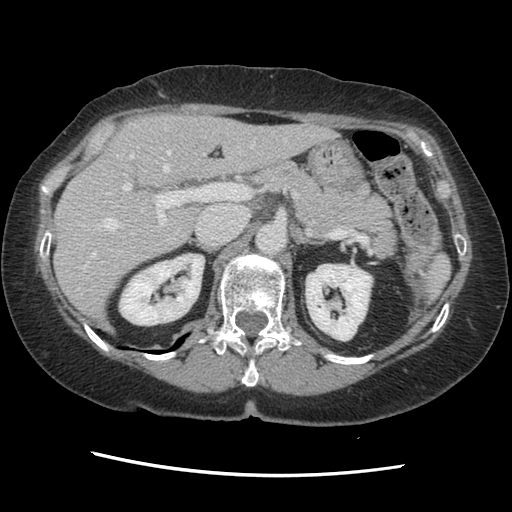
Contrast-enhanced abdominal CT, one axial slice; slice 85 of 141 in the series (ordered by position); 120 kVp; soft-tissue window (W 400 / L 40 HU); 2.5 mm slice thickness; 512 × 512 image matrix, field of view 330 × 330 mm. Female patient, age 61 years. Case-level facts recorded for this patient, not image findings: diagnosis: colorectal cancer liver metastases, imaged before liver resection.
Structures marked on this image (manually delineated by an expert):
- hepatic veins: bounding box [x1, y1, x2, y2] px = [82, 127, 287, 270]
- liver: [56, 114, 331, 316]
- planned liver remnant (the part of the liver to remain after resection): [56, 114, 331, 316]
- portal vein (with intrahepatic branches): [109, 153, 243, 226]